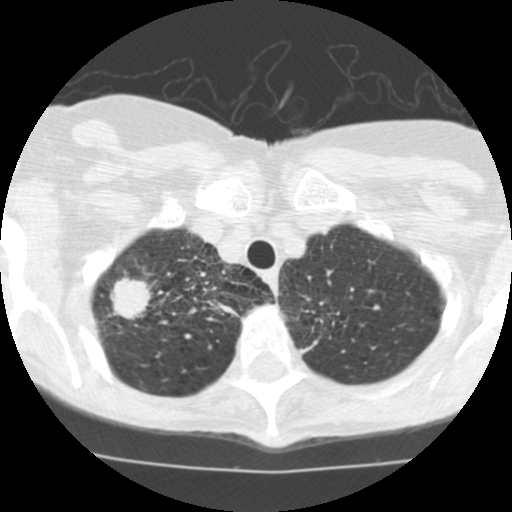
Axial slice from a low-dose chest CT screening exam, second screening round (one year after baseline), lung window (W 1500 / L -600 HU), 2.5 mm slice thickness, slice 17 of 115 in the series. Female participant, aged 68 years at enrolment. Current smoker at enrolment.
- Lesion marked by an expert reader, box from (x=94, y=265) to (x=159, y=336) px.
- The screening reader recorded 3 non-calcified nodules or masses ≥4 mm on this exam (right upper lobe, right upper lobe, right middle lobe); which of them this box marks is not recorded.
- Participant outcome: lung cancer diagnosed 36 days after this screen — large cell neuroendocrine carcinoma, right upper lobe, undifferentiated (G4), stage IB (AJCC 6th edition), 22 mm at pathology.